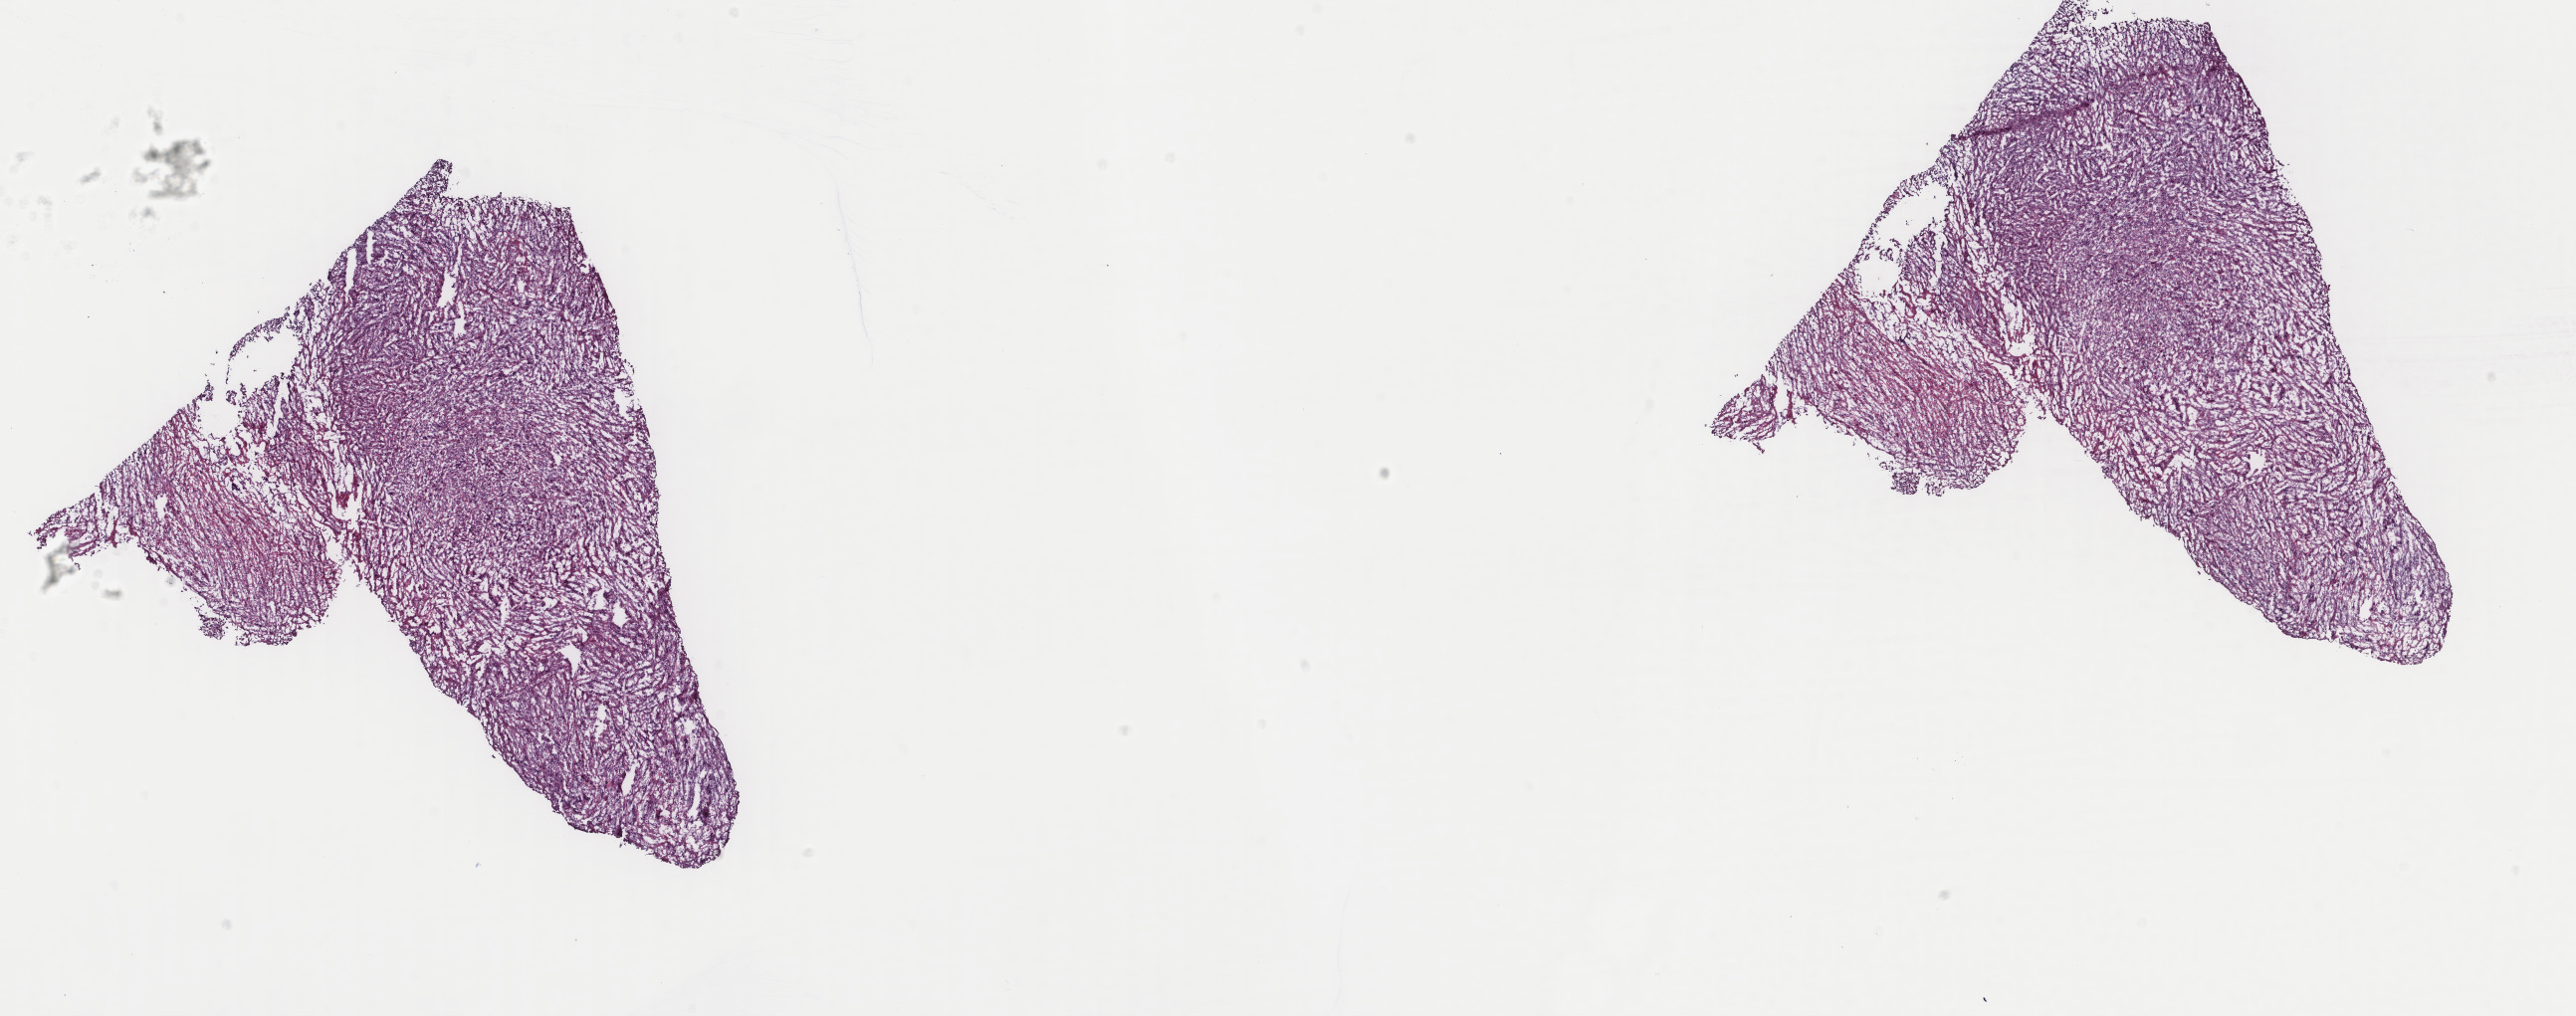
Digitized H&E tissue section (whole slide), a low-resolution overview of the entire scanned area, about 20.5 x 8.1 mm; frozen section from the top of the tissue portion; sample: primary tumour, uterus. Patient: female, age at initial diagnosis 69 years. Composition of this section per pathologist review: tumour cells 85%, tumour nuclei 100%.
Diagnosis: Leiomyosarcoma, NOS.